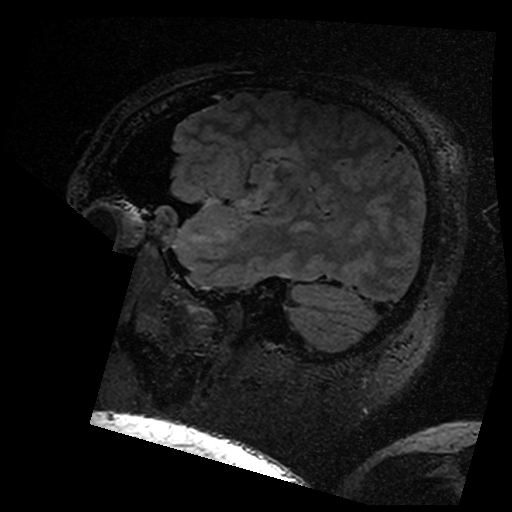
Brain MRI from a brain-tumour surgery series, one sagittal slice. Slice 132 of 176 in the series (ordered by position). T2 FLAIR. 1 mm slice thickness. 512 × 512 image matrix. Case-level facts recorded for this patient, not image findings: histopathology: Astrocytoma; WHO grade: 3; IDH mutation: yes.
Structures marked on this image (expert manual segmentation):
- residual tumour: bounding box (x1, y1, x2, y2) in pixels: (278, 154, 290, 164)